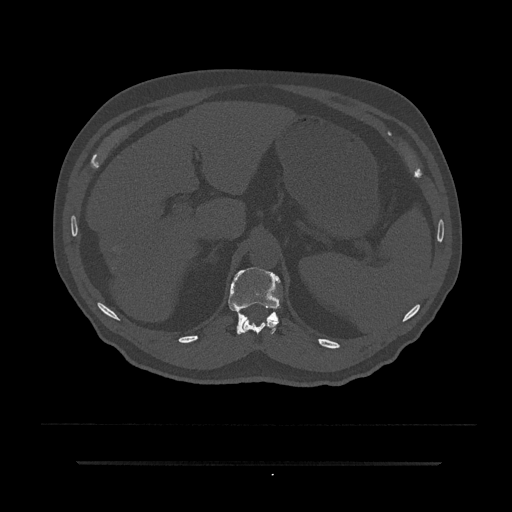
CT including the spine, one axial slice. Position 237 of 797 along the scan axis. Reconstruction kernel Br40s/3. Bone window (W 1800 / L 400 HU). 0.5 mm slice thickness. 512 × 512 image matrix. Patient: male, 59 years. Case-level facts recorded for this patient, not image findings: primary cancer: bile ducts; vertebrae with lytic lesions (as recorded): T10.
Structures marked on this image (semi-automatically segmented with operator editing):
- T11 vertebra: bounding box (x1, y1, x2, y2) in pixels: (242, 319, 279, 335)
- T12 vertebra: (228, 267, 280, 335)